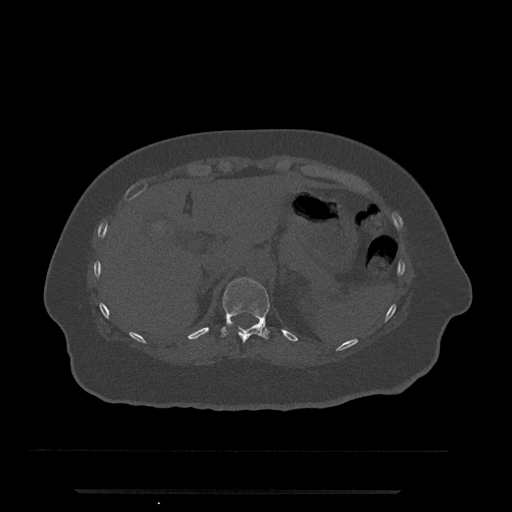
CT including the spine, one axial slice; slice 227 of 797 in the series (ordered by position); reconstruction kernel Br40s/3; 120 kVp; bone window (W 1800 / L 400 HU); 0.5 mm slice thickness; 512 × 512 image matrix. Female patient, age 51 years. Case-level facts recorded for this patient, not image findings: primary cancer: neuro; vertebrae with lytic lesions (as recorded): T8.
Structures marked on this image (semi-automatically segmented with operator editing):
- T11 vertebra: box from (x=221, y=277) to (x=270, y=343) px